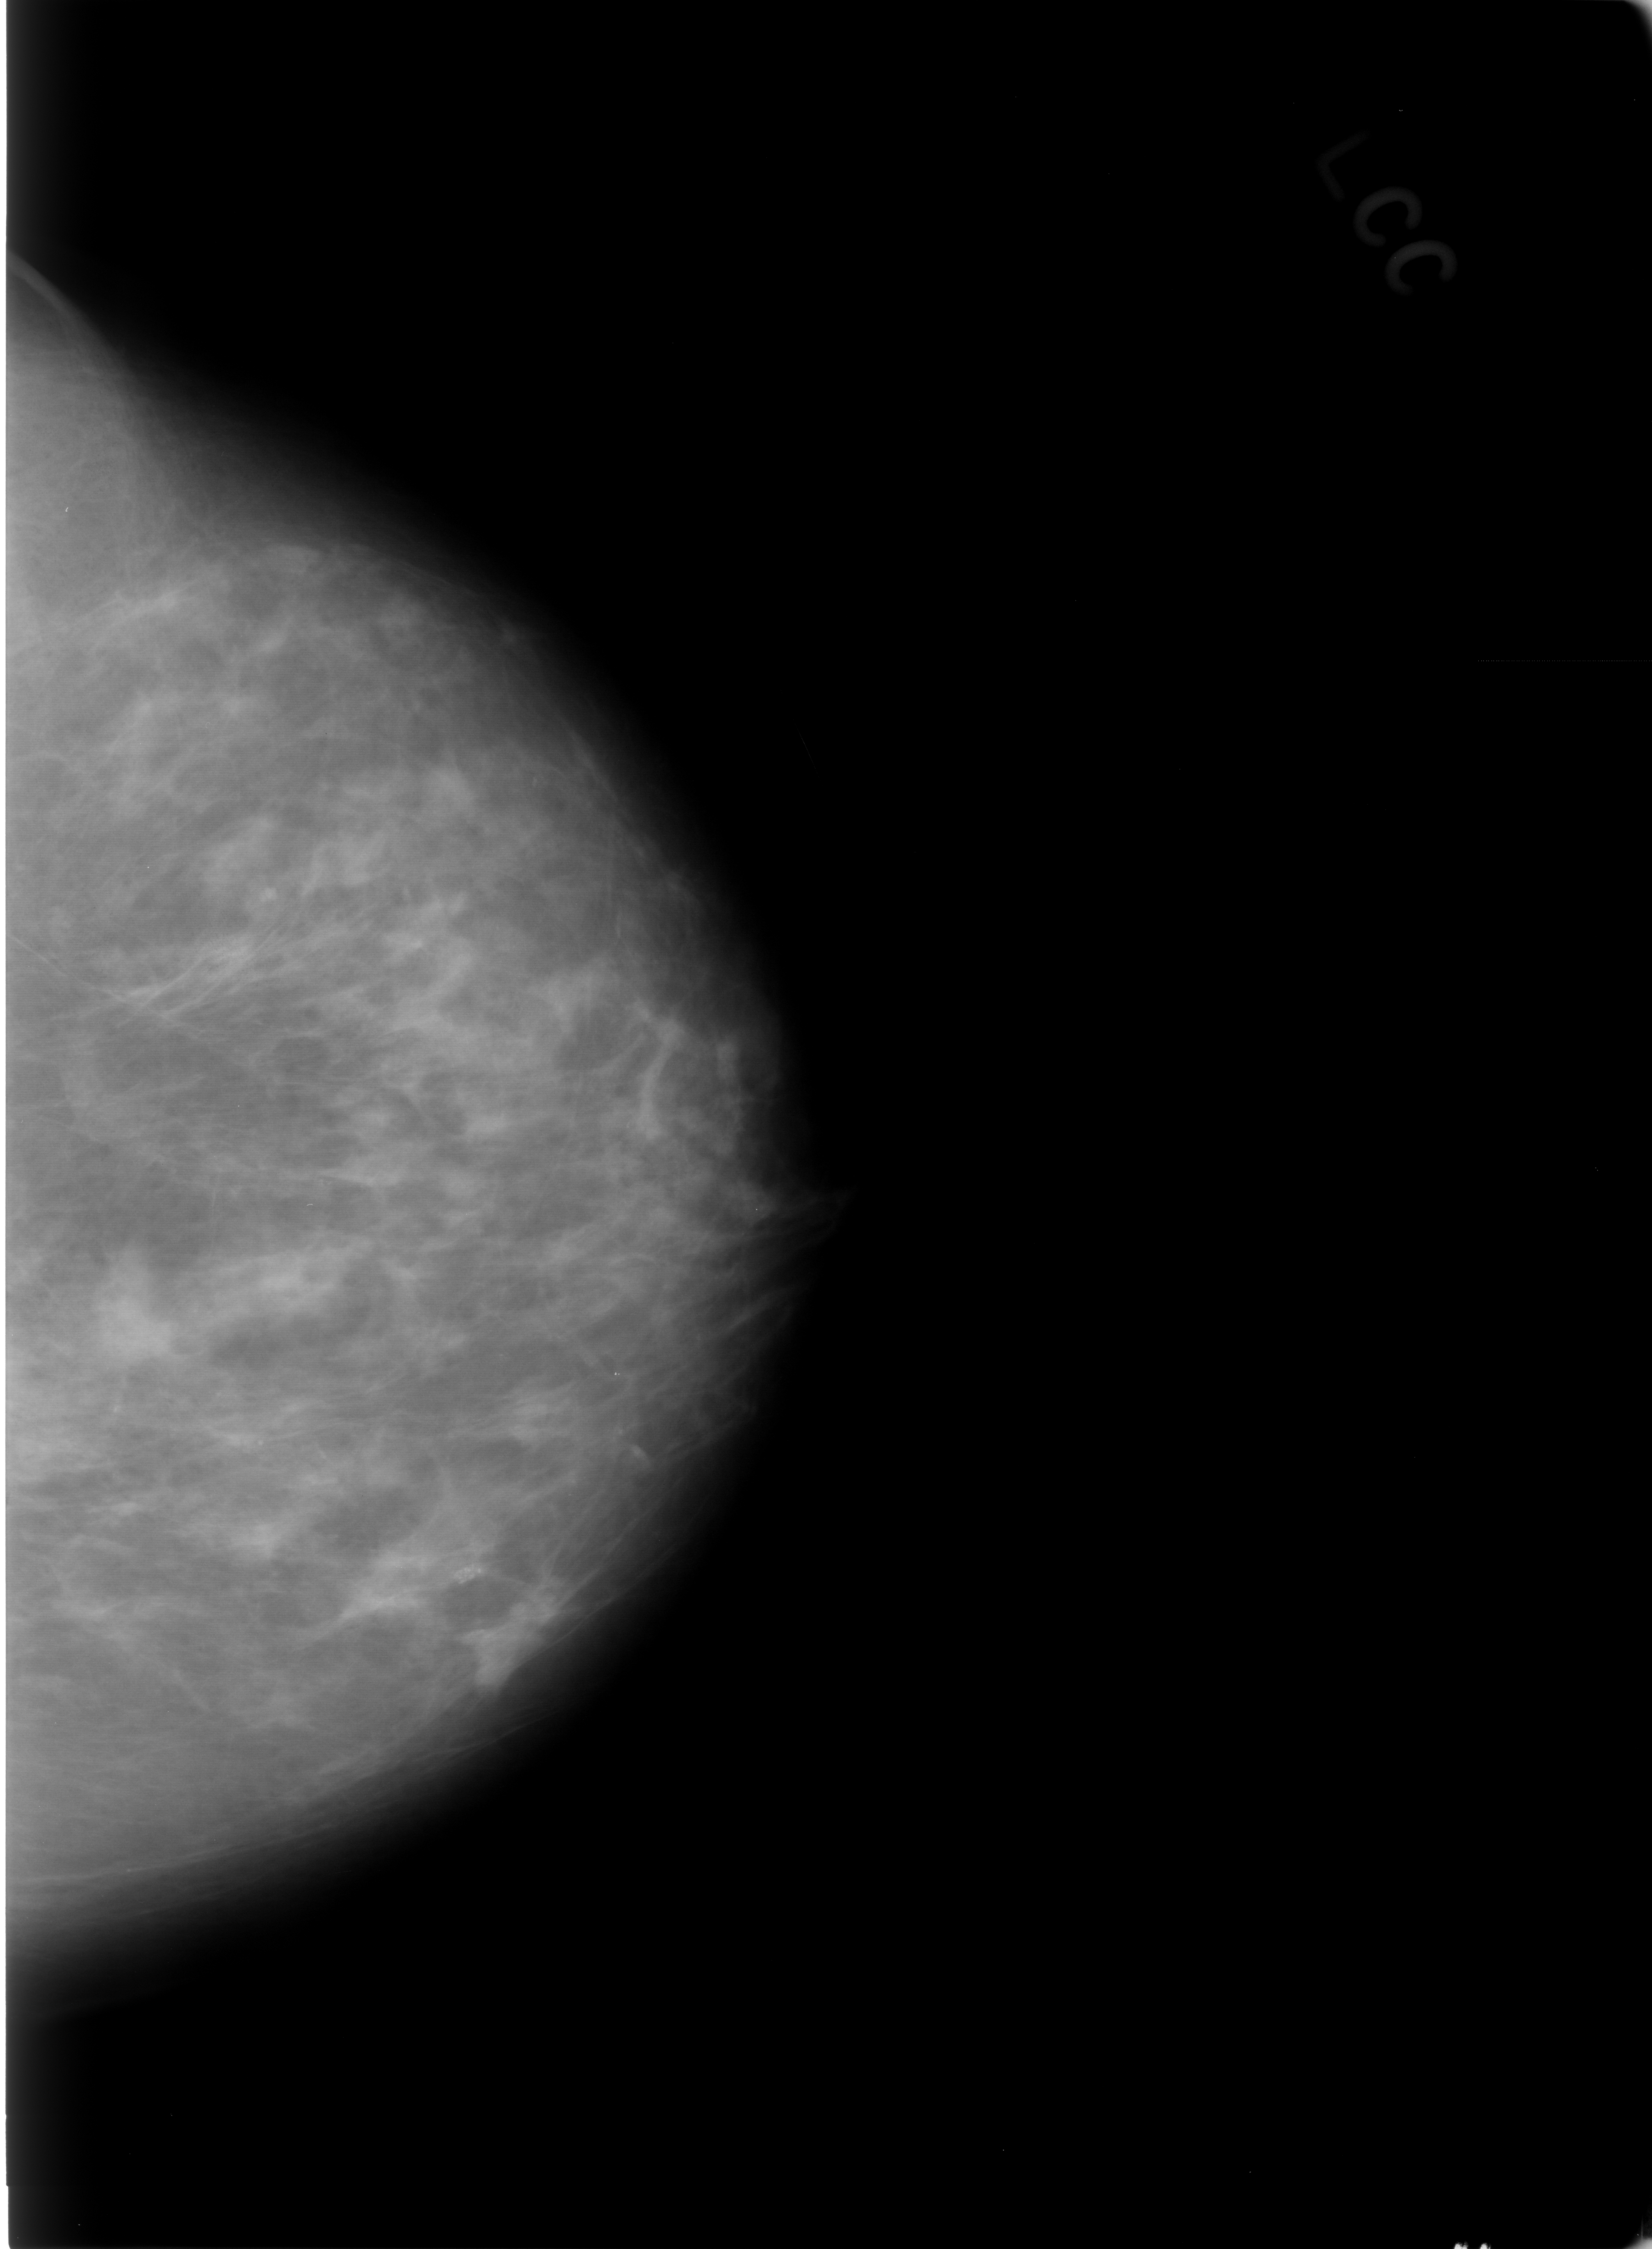
Digitized screen-film mammogram; left breast; craniocaudal (CC) view; breast composition: scattered fibroglandular densities (BI-RADS density category 2 of 4); 1652 × 2249 image matrix.
Expert-marked regions of interest on this film, with their recorded descriptors:
- calcifications, morphology pleomorphic, distribution clustered; BI-RADS assessment category 4; pathology result (as recorded, not read from the image): benign: box from (x=415, y=1496) to (x=529, y=1641) px